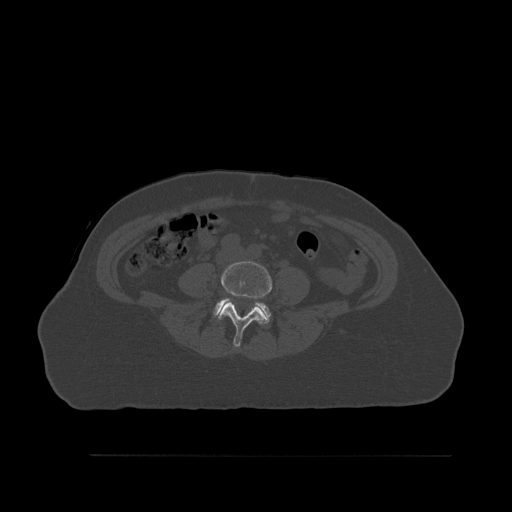
CT including the spine, one axial slice. Position 202 of 527 along the scan axis. Bone window (W 1800 / L 400 HU). 1.5 mm slice thickness. 512 × 512 image matrix. Patient: female, 73 years. Case-level facts recorded for this patient, not image findings: primary cancer: breast.
Outlined on this slice (semi-automatically segmented with operator editing):
- L4 vertebra: box from (x=218, y=261) to (x=272, y=347) px
- L5 vertebra: (x=213, y=298)–(x=271, y=325)